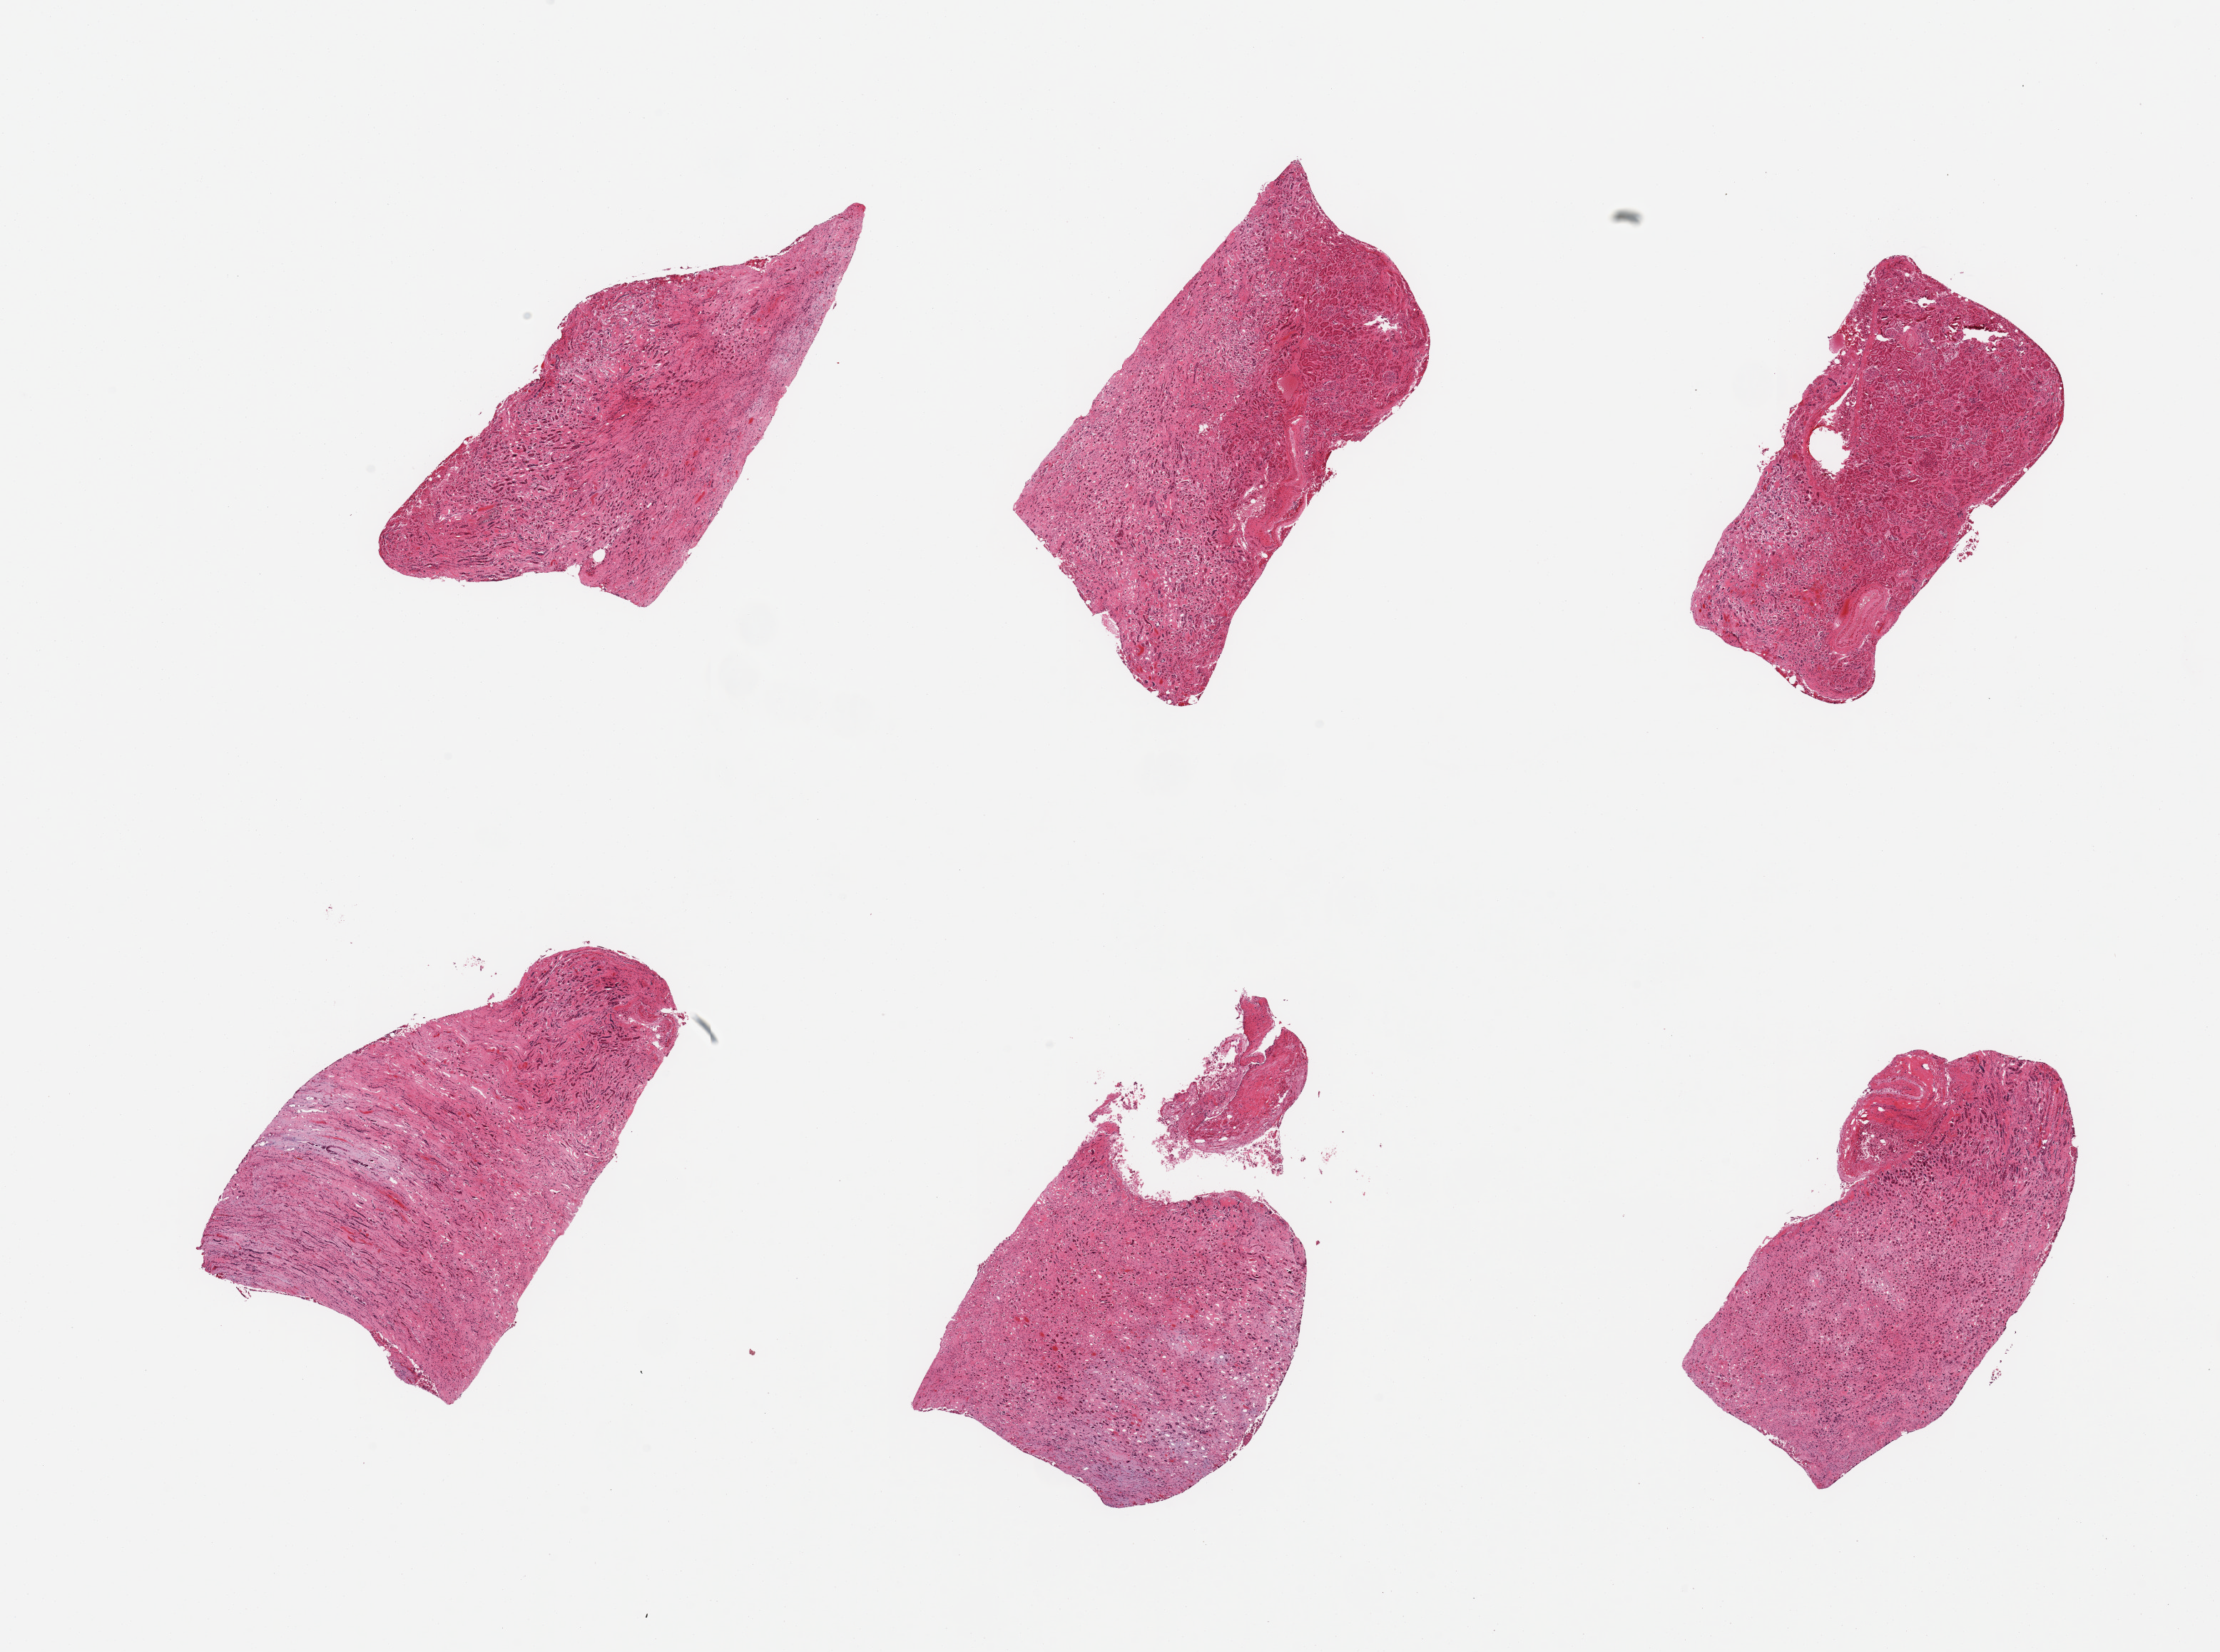
Hematoxylin and eosin (H&E) whole-slide image, whole scanned area (about 24.6 x 18.3 mm) shown as a low-resolution overview, PAXgene-fixed paraffin-embedded (PFPE) section, sampled site (target tissue): renal cortex, tissue donor sample.
Pathologist's review note for this sample: 6 pieces; only two pieces contain renal cortex.